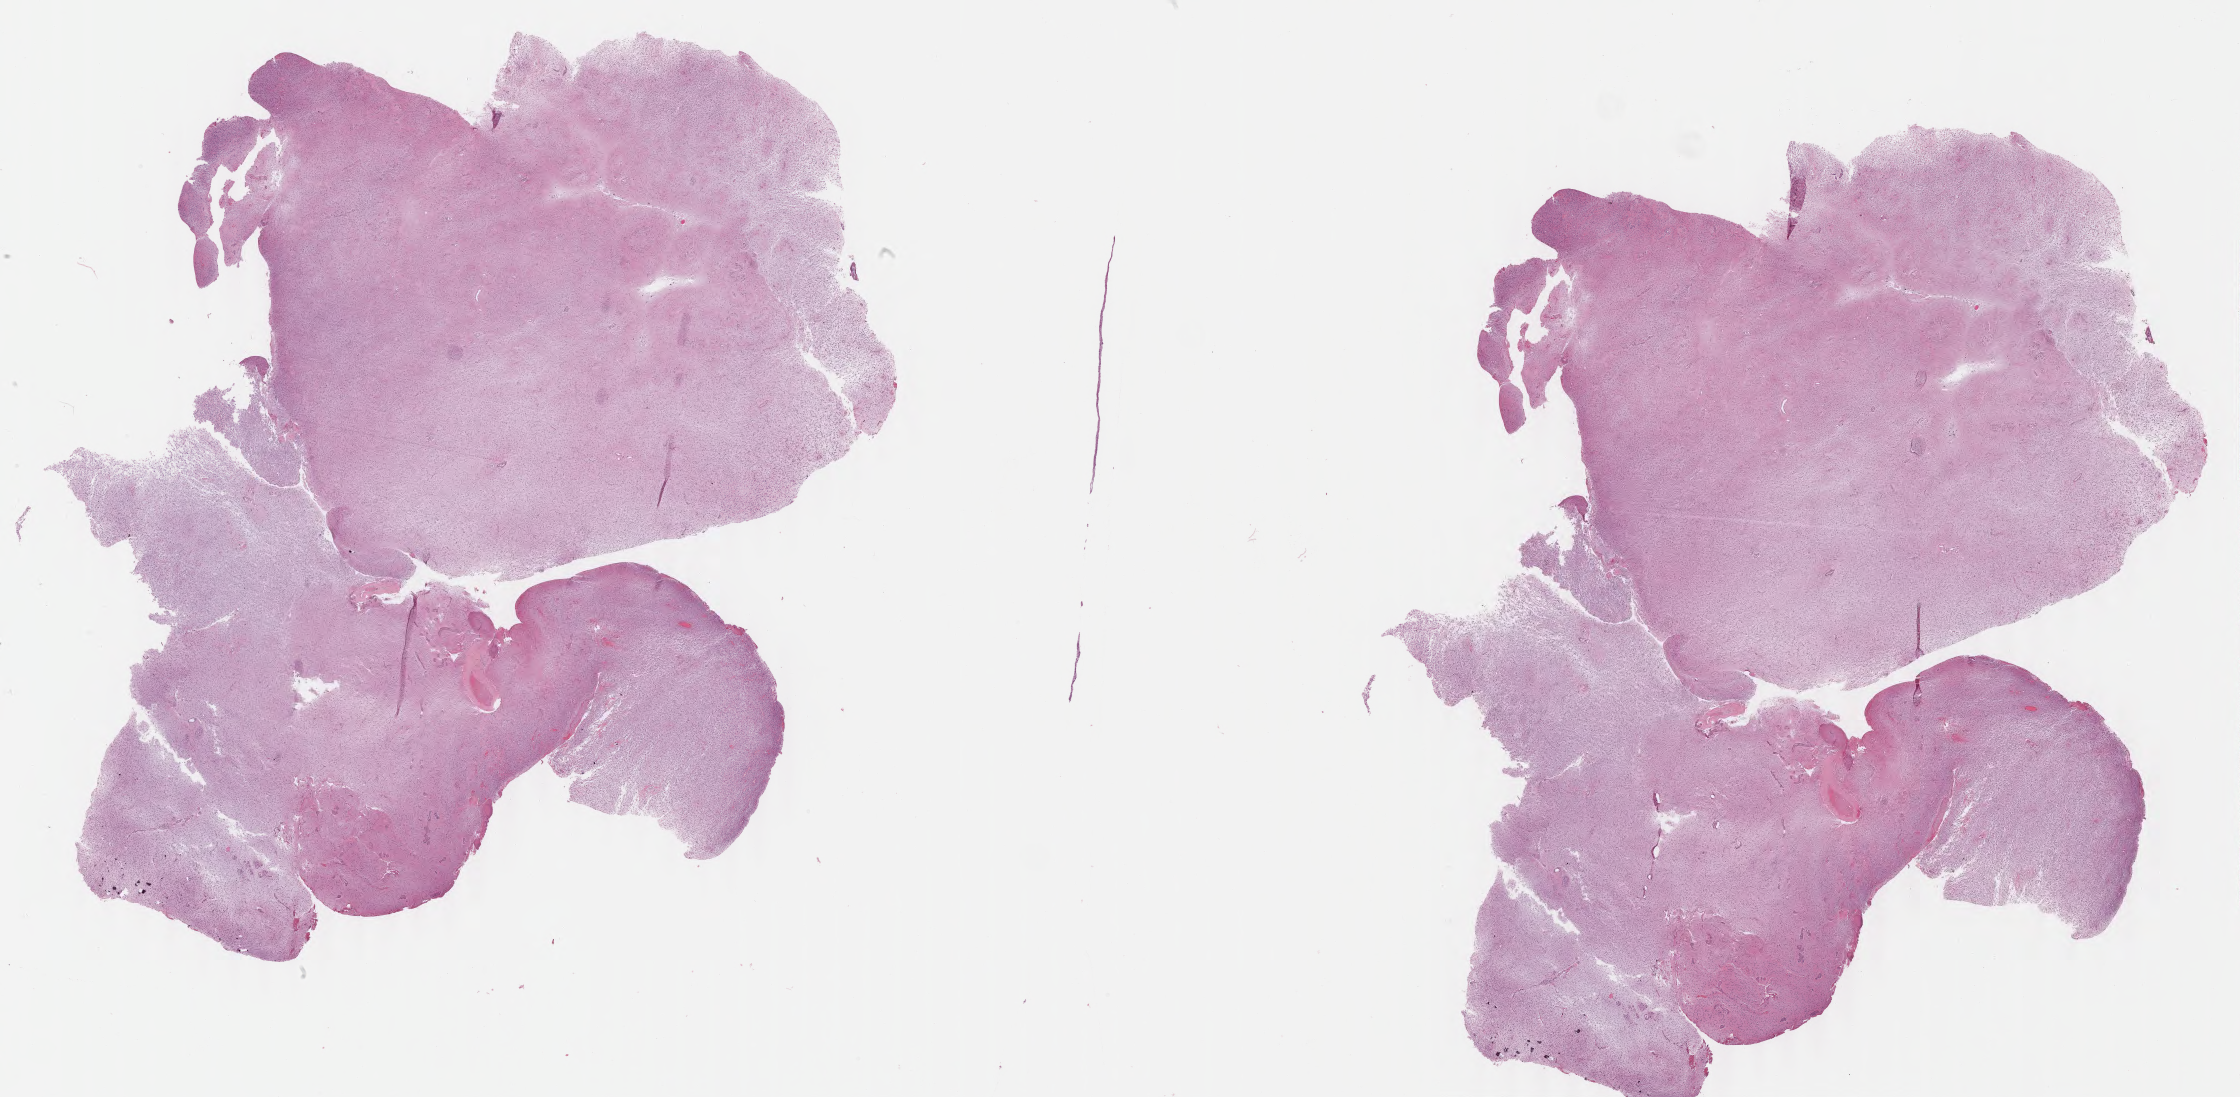
Hematoxylin and eosin (H&E) stained whole-slide image — a low-resolution overview of the entire scanned area, about 35.4 x 17.3 mm (slide scanned at 40x); FFPE section; brain, primary tumour sample. Male, age 29 years at initial diagnosis.
Diagnosis: Astrocytoma, anaplastic (cerebrum).